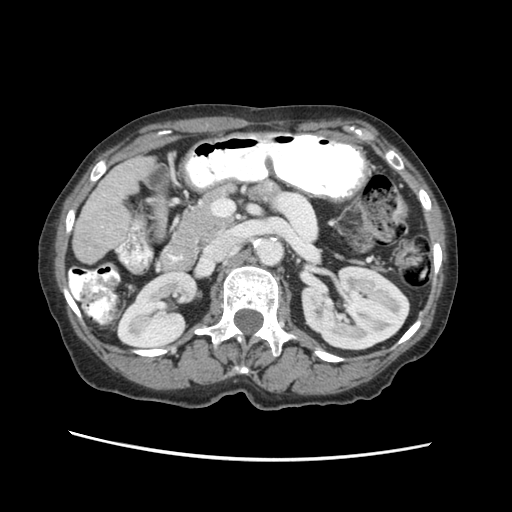
Contrast-enhanced abdominal CT (liver protocol), one axial slice. Slice 15 of 63 in the series (ordered by position). Soft-tissue window (W 400 / L 40 HU). 2.5 mm slice thickness. 512 × 512 image matrix, field of view 340 × 340 mm. From the clinical record (not read from this slice): diagnosis: hepatocellular carcinoma (patient treated with transarterial chemoembolisation; whether this scan precedes or follows treatment is not stated here); TNM stage (as recorded): Stage-I; Child-Pugh class: B; tumour differentiation: well differentiated; tumour nodularity: uninodular.
Outlined on this slice (semi-automatic segmentation, software-assisted and operator-edited):
- liver parenchyma outside the tumour (the mass and vessels are separate outlines, so this box may not span the whole liver): box from (x=72, y=154) to (x=153, y=262) px